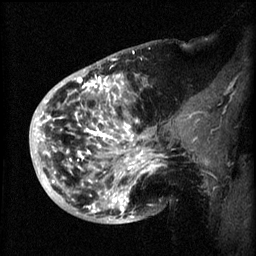
Breast MRI (dynamic contrast-enhanced), one sagittal slice; position 20 of 60 along the scan axis; 3 images stored at this slice position (order not interpretable as contrast timing); 1.5 T; TE 4.2 ms, TR 8.2 ms; 256 × 256 image matrix, field of view 200 × 200 mm. Patient: female, 50 years.
Outlined on this slice (semi-automatically segmented with operator editing):
- analysis volume of interest (the breast-tissue region the enhancement analysis was run in; not a lesion): bounding box [x1, y1, x2, y2] px = [44, 72, 173, 219]
- tumour enhancement mask (voxels above the 70 % enhancement threshold inside the analysis volume of interest): [44, 76, 163, 219]